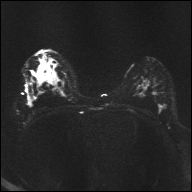
Breast MRI, one axial slice; diffusion-weighted series; image 2 of 4 stored at this slice position (different b-values; order by instance number); 1.5 T; 192 × 192 image matrix. Female patient.
Annotated regions visible in this slice (outlined manually by an expert reader):
- tumour on diffusion-weighted imaging: bounding box (x1, y1, x2, y2) in pixels: (39, 64, 52, 82)